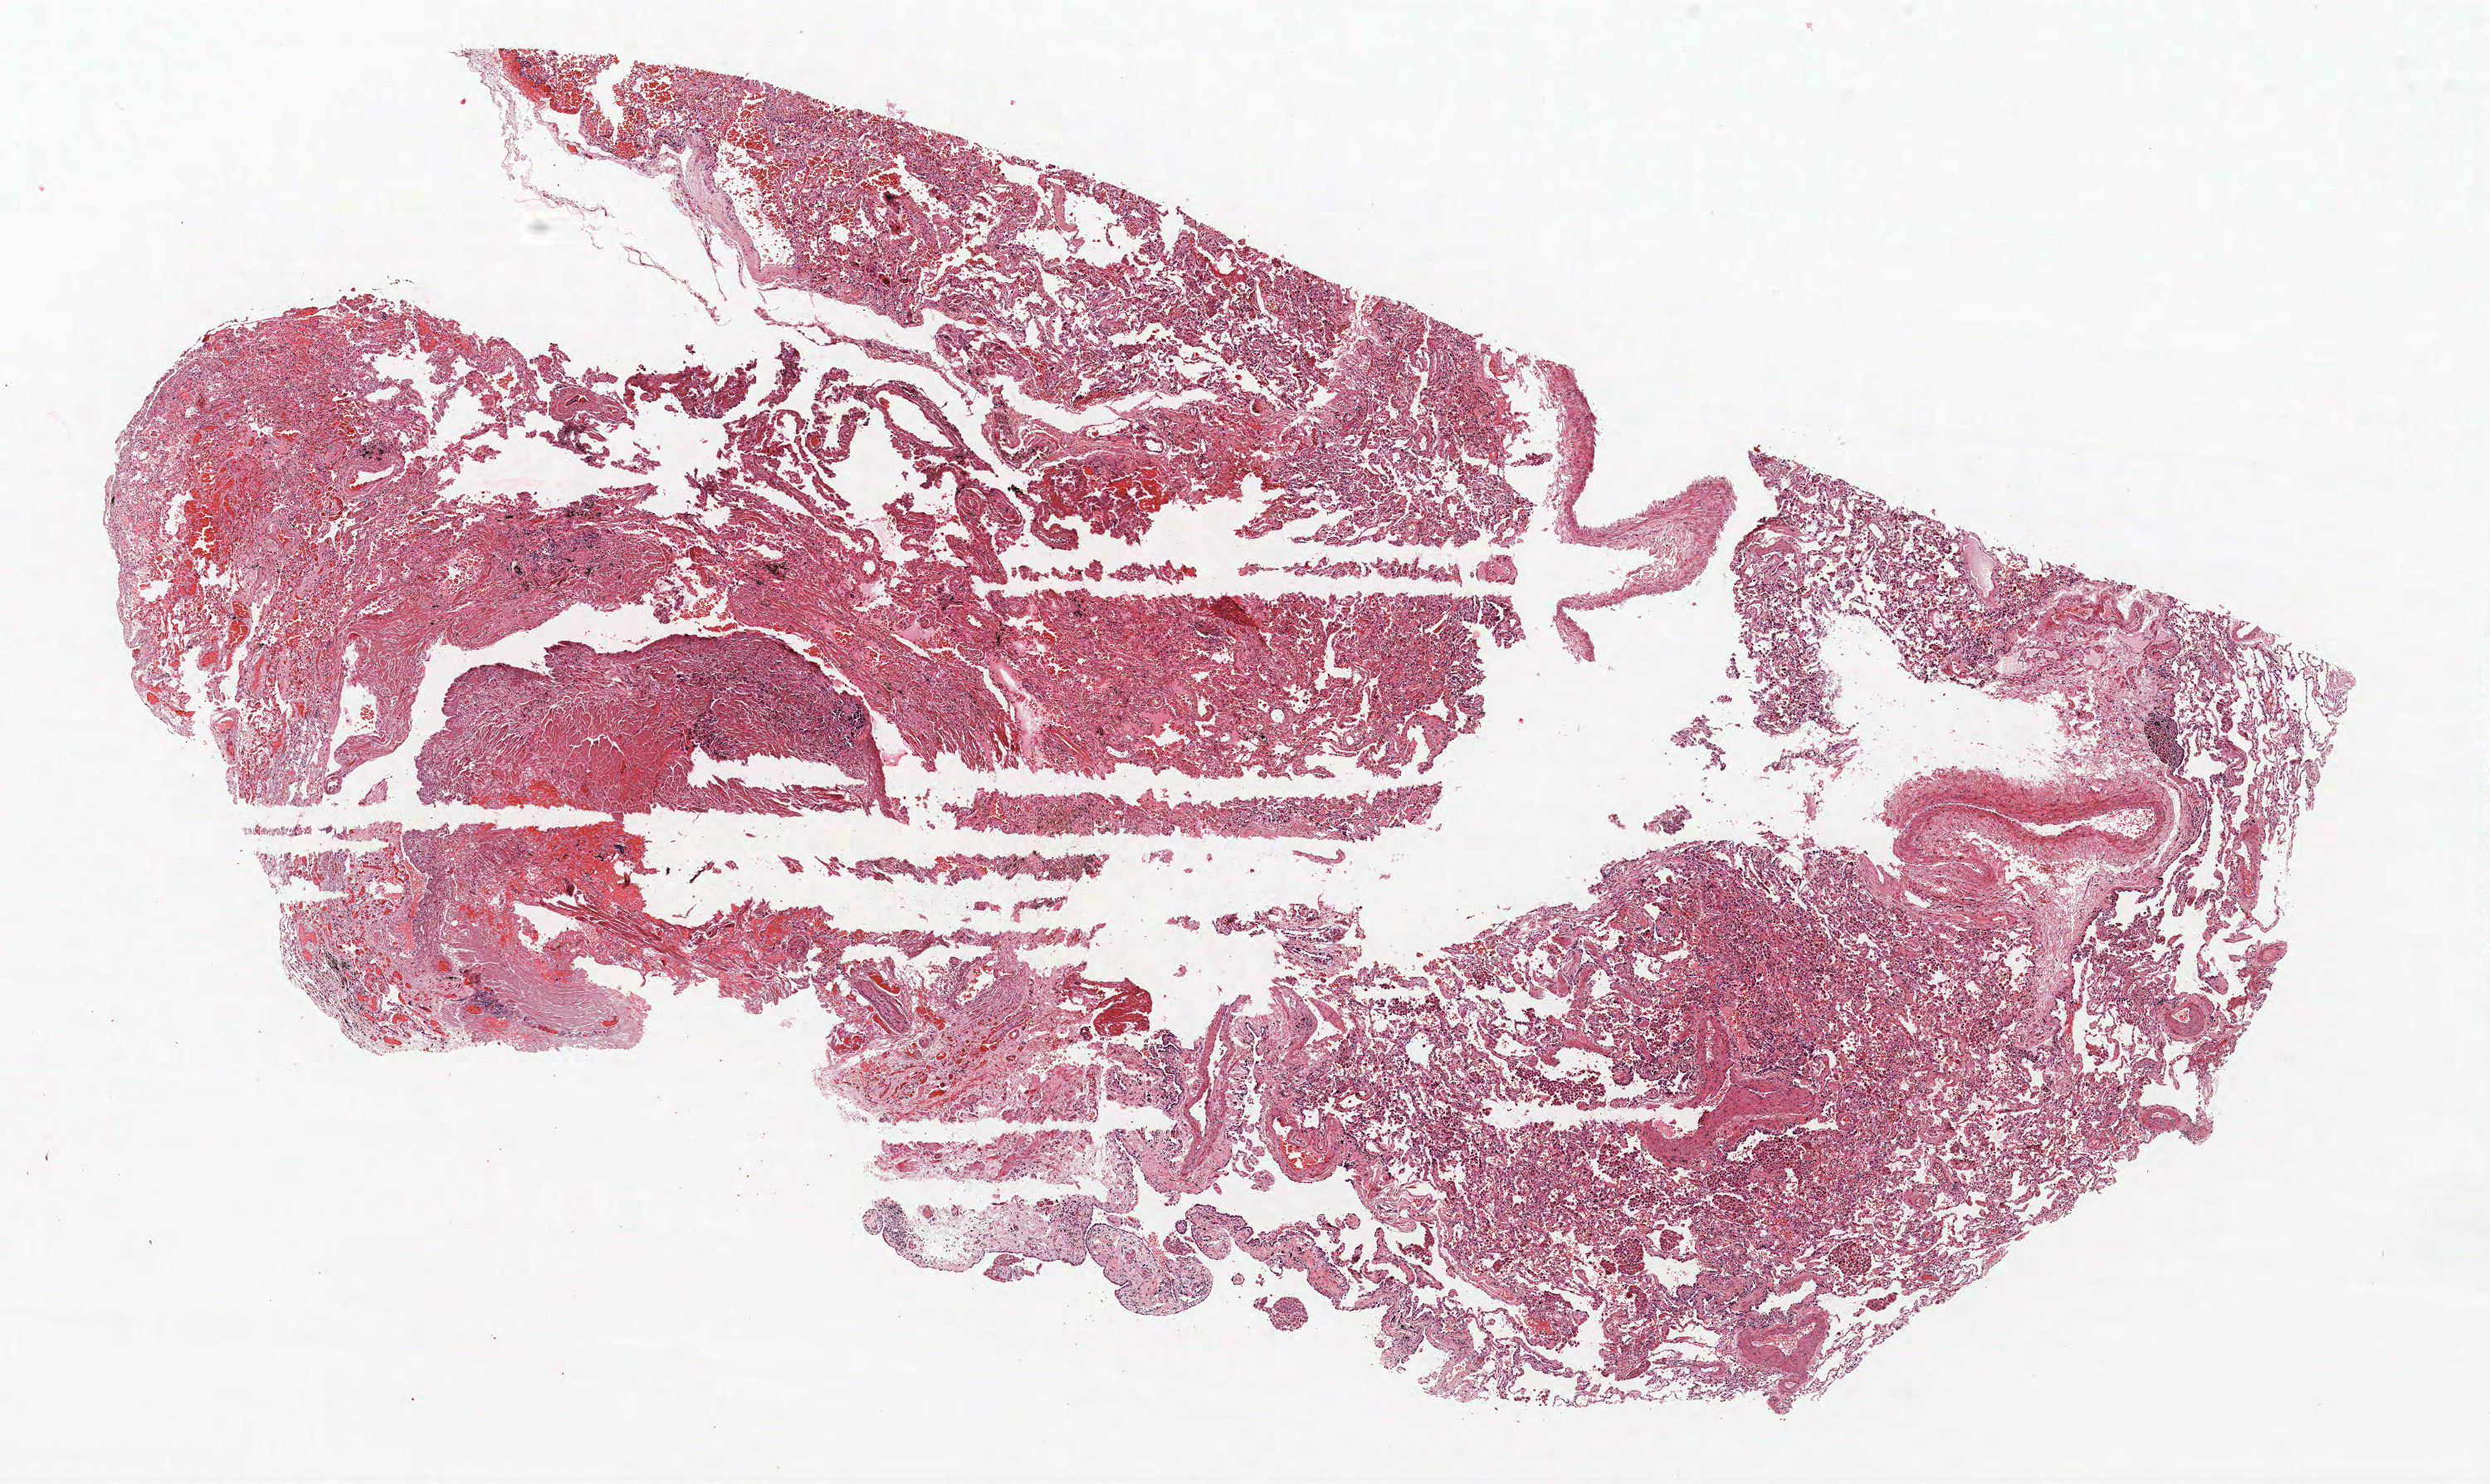
Whole-slide histology image, Hematoxylin and eosin (H&E) stained, shown as a low-resolution overview of the whole scanned area (about 12.0 x 7.2 mm). FFPE section. Lung tissue. Female, age 55 at enrolment. Current smoker at enrolment. Grade: moderately differentiated (G2).
Participant's lung-cancer diagnosis: Bronchiolo-alveolar adenocarcinoma, NOS. Stage (AJCC 6th edition): IIA. Primary tumour location (clinical record): right upper lobe. ICD-O-3 topography: upper lobe of lung (C34.1). Tumour size (pathology): 13 mm.